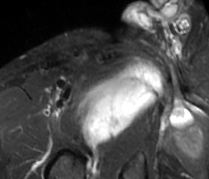
MRI of an extremity soft-tissue mass, one axial slice. Position 69 of 89 along the scan axis. STIR. MR volume resampled by the dataset authors to the PET/CT grid (not the native acquisition matrix). 3.27 mm slice thickness. 209 × 179 image matrix, field of view 204 × 175 mm. Male patient. Case-level facts recorded for this patient, not image findings: histological type: undifferentiated - pleiomorphic; grade: high; site of the primary tumour: right thigh.
Structures marked on this image (expert contour drawn on MRI and transferred to this co-registered scan by the dataset authors):
- gross tumour volume including surrounding oedema: bounding box (x1, y1, x2, y2) in pixels: (80, 62, 163, 147)
- gross tumour volume (mass): (80, 66, 161, 145)